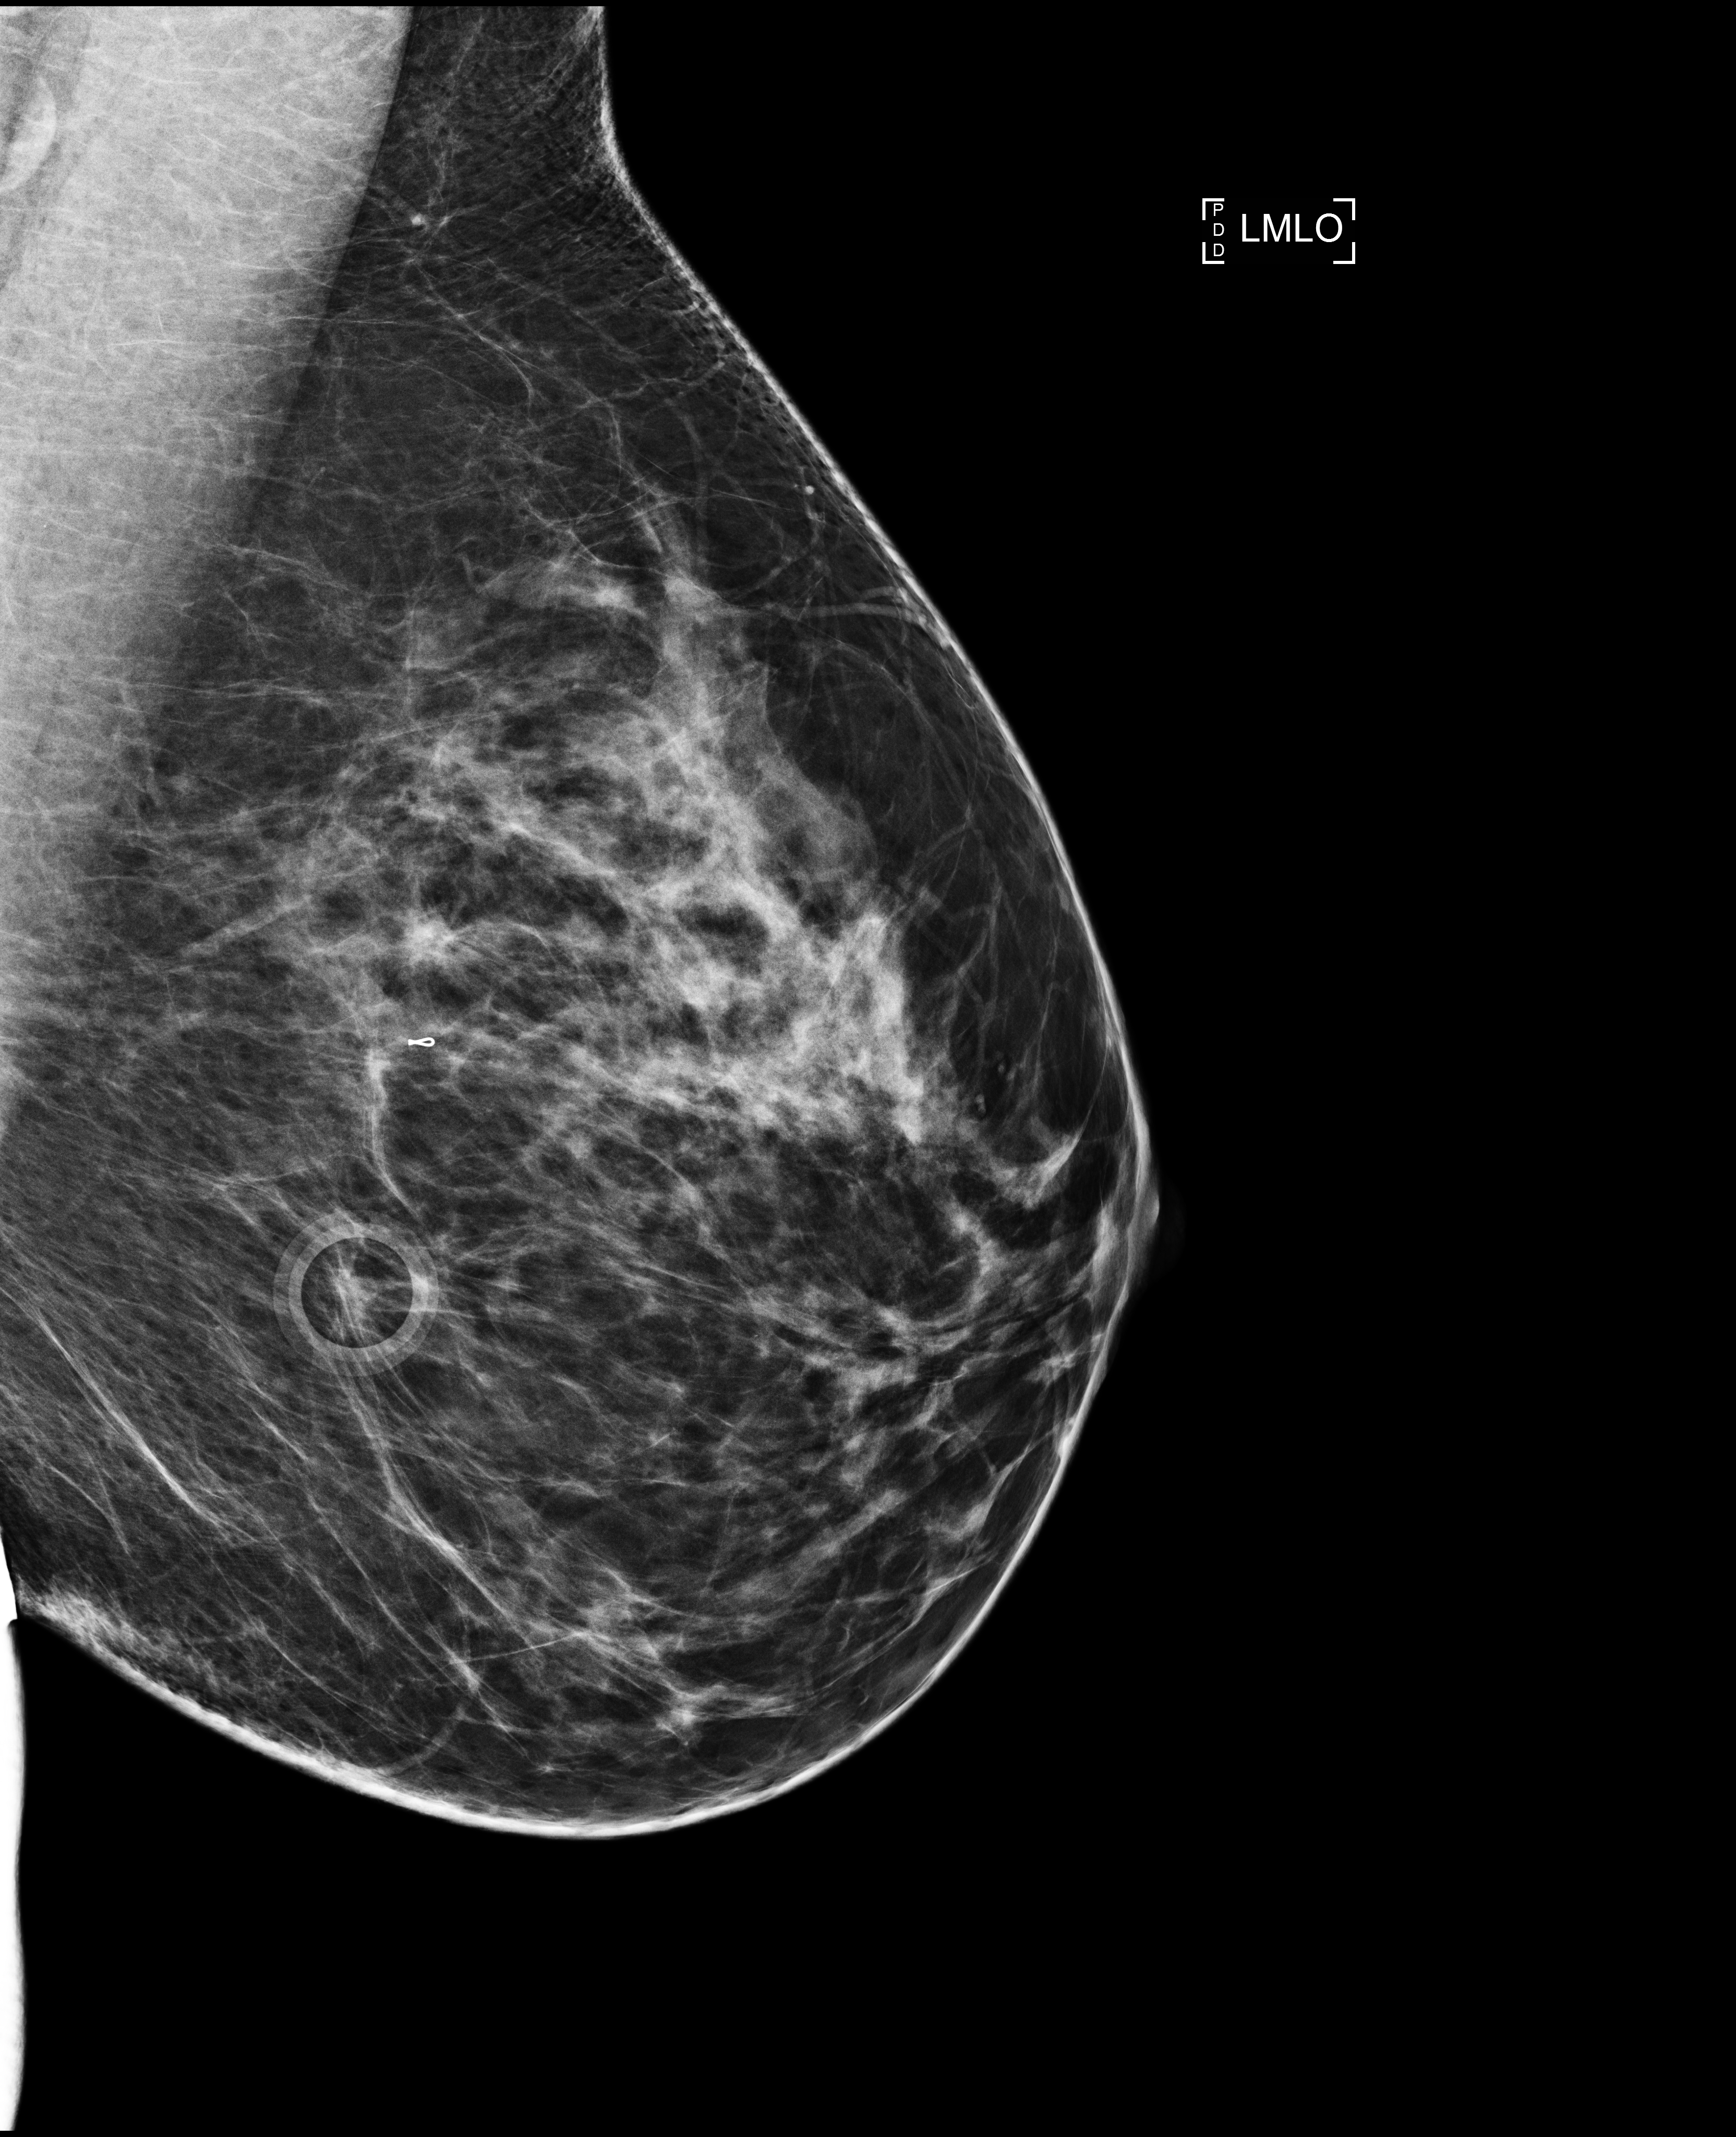
Screening examination. Patient aged 51 years (female).
Image type: full-field digital mammogram. Breast: left. Projection: mediolateral oblique (MLO) view.